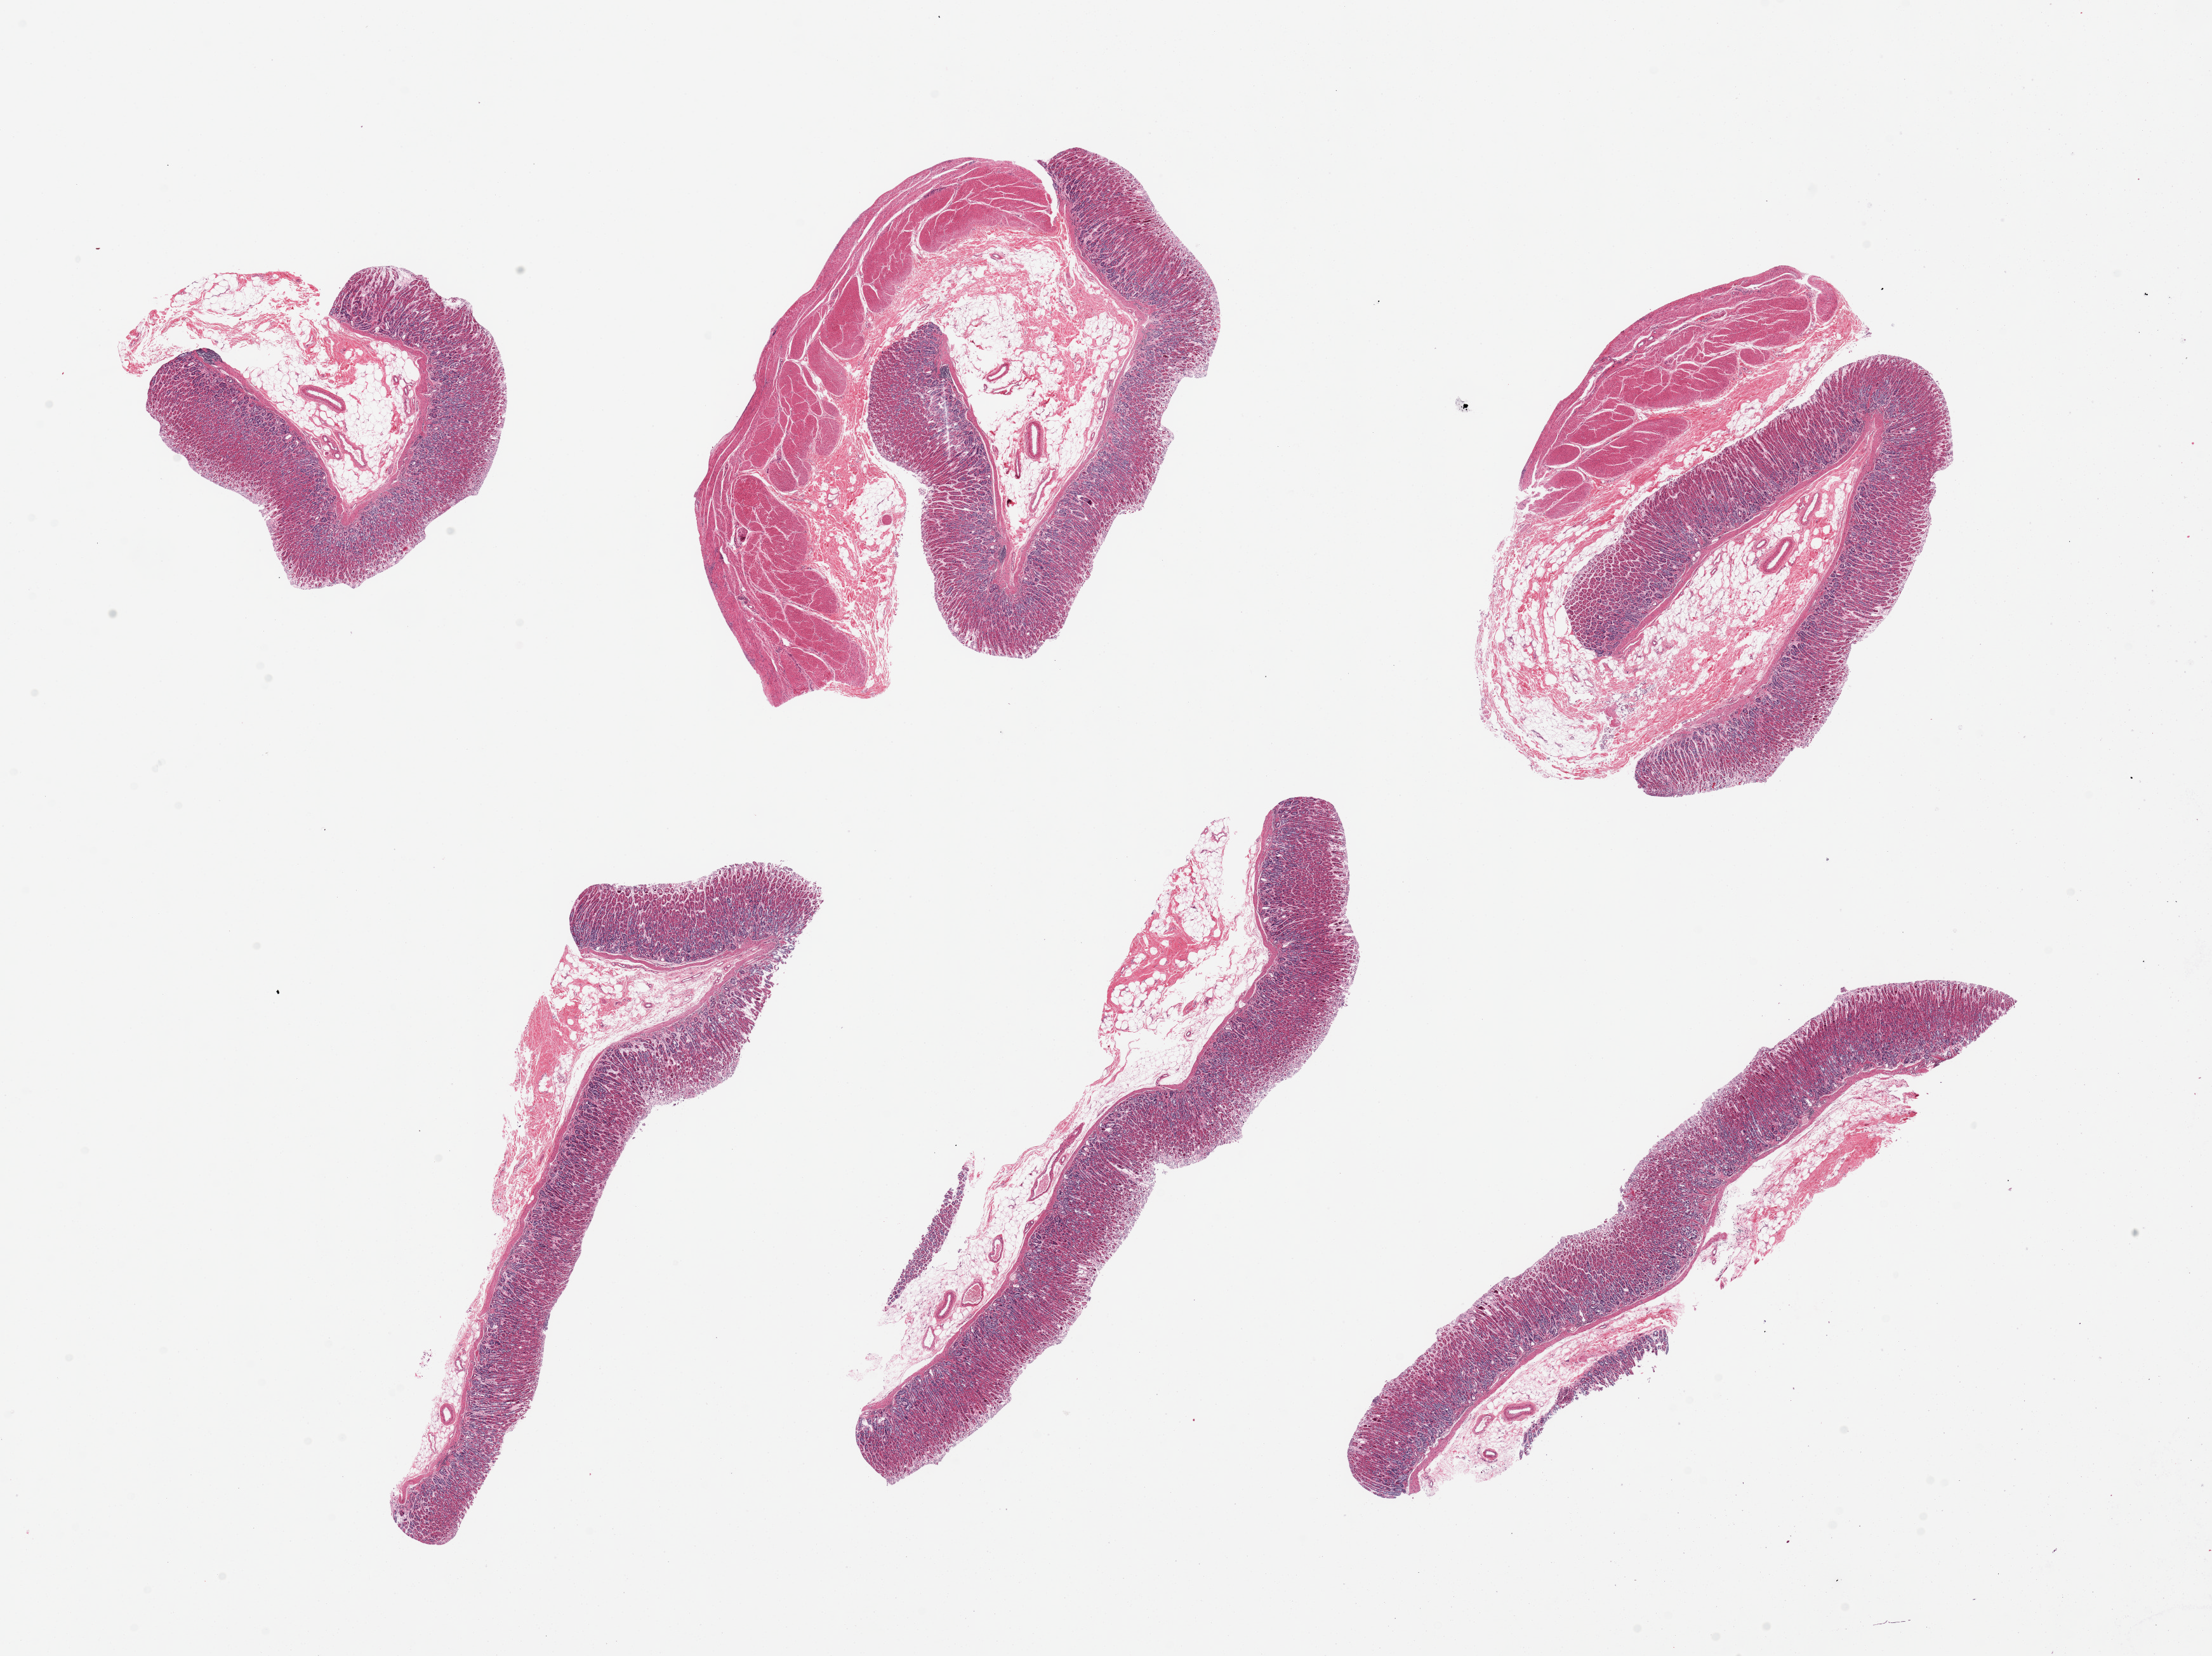
Haematoxylin and eosin whole-slide image — low-resolution overview of the scanned area, about 27.6 x 20.6 mm (acquisition: 20x scan); PAXgene-fixed, paraffin-embedded tissue; sampled site (target tissue): stomach; tissue donor sample. Donor: male.
• reviewer comment on this tissue sample: 6 pieces, mucosa reasonably well preserved; some areas approach score '2' along luminal surface. Mucosa is ~1mm/ ~50% total thickness